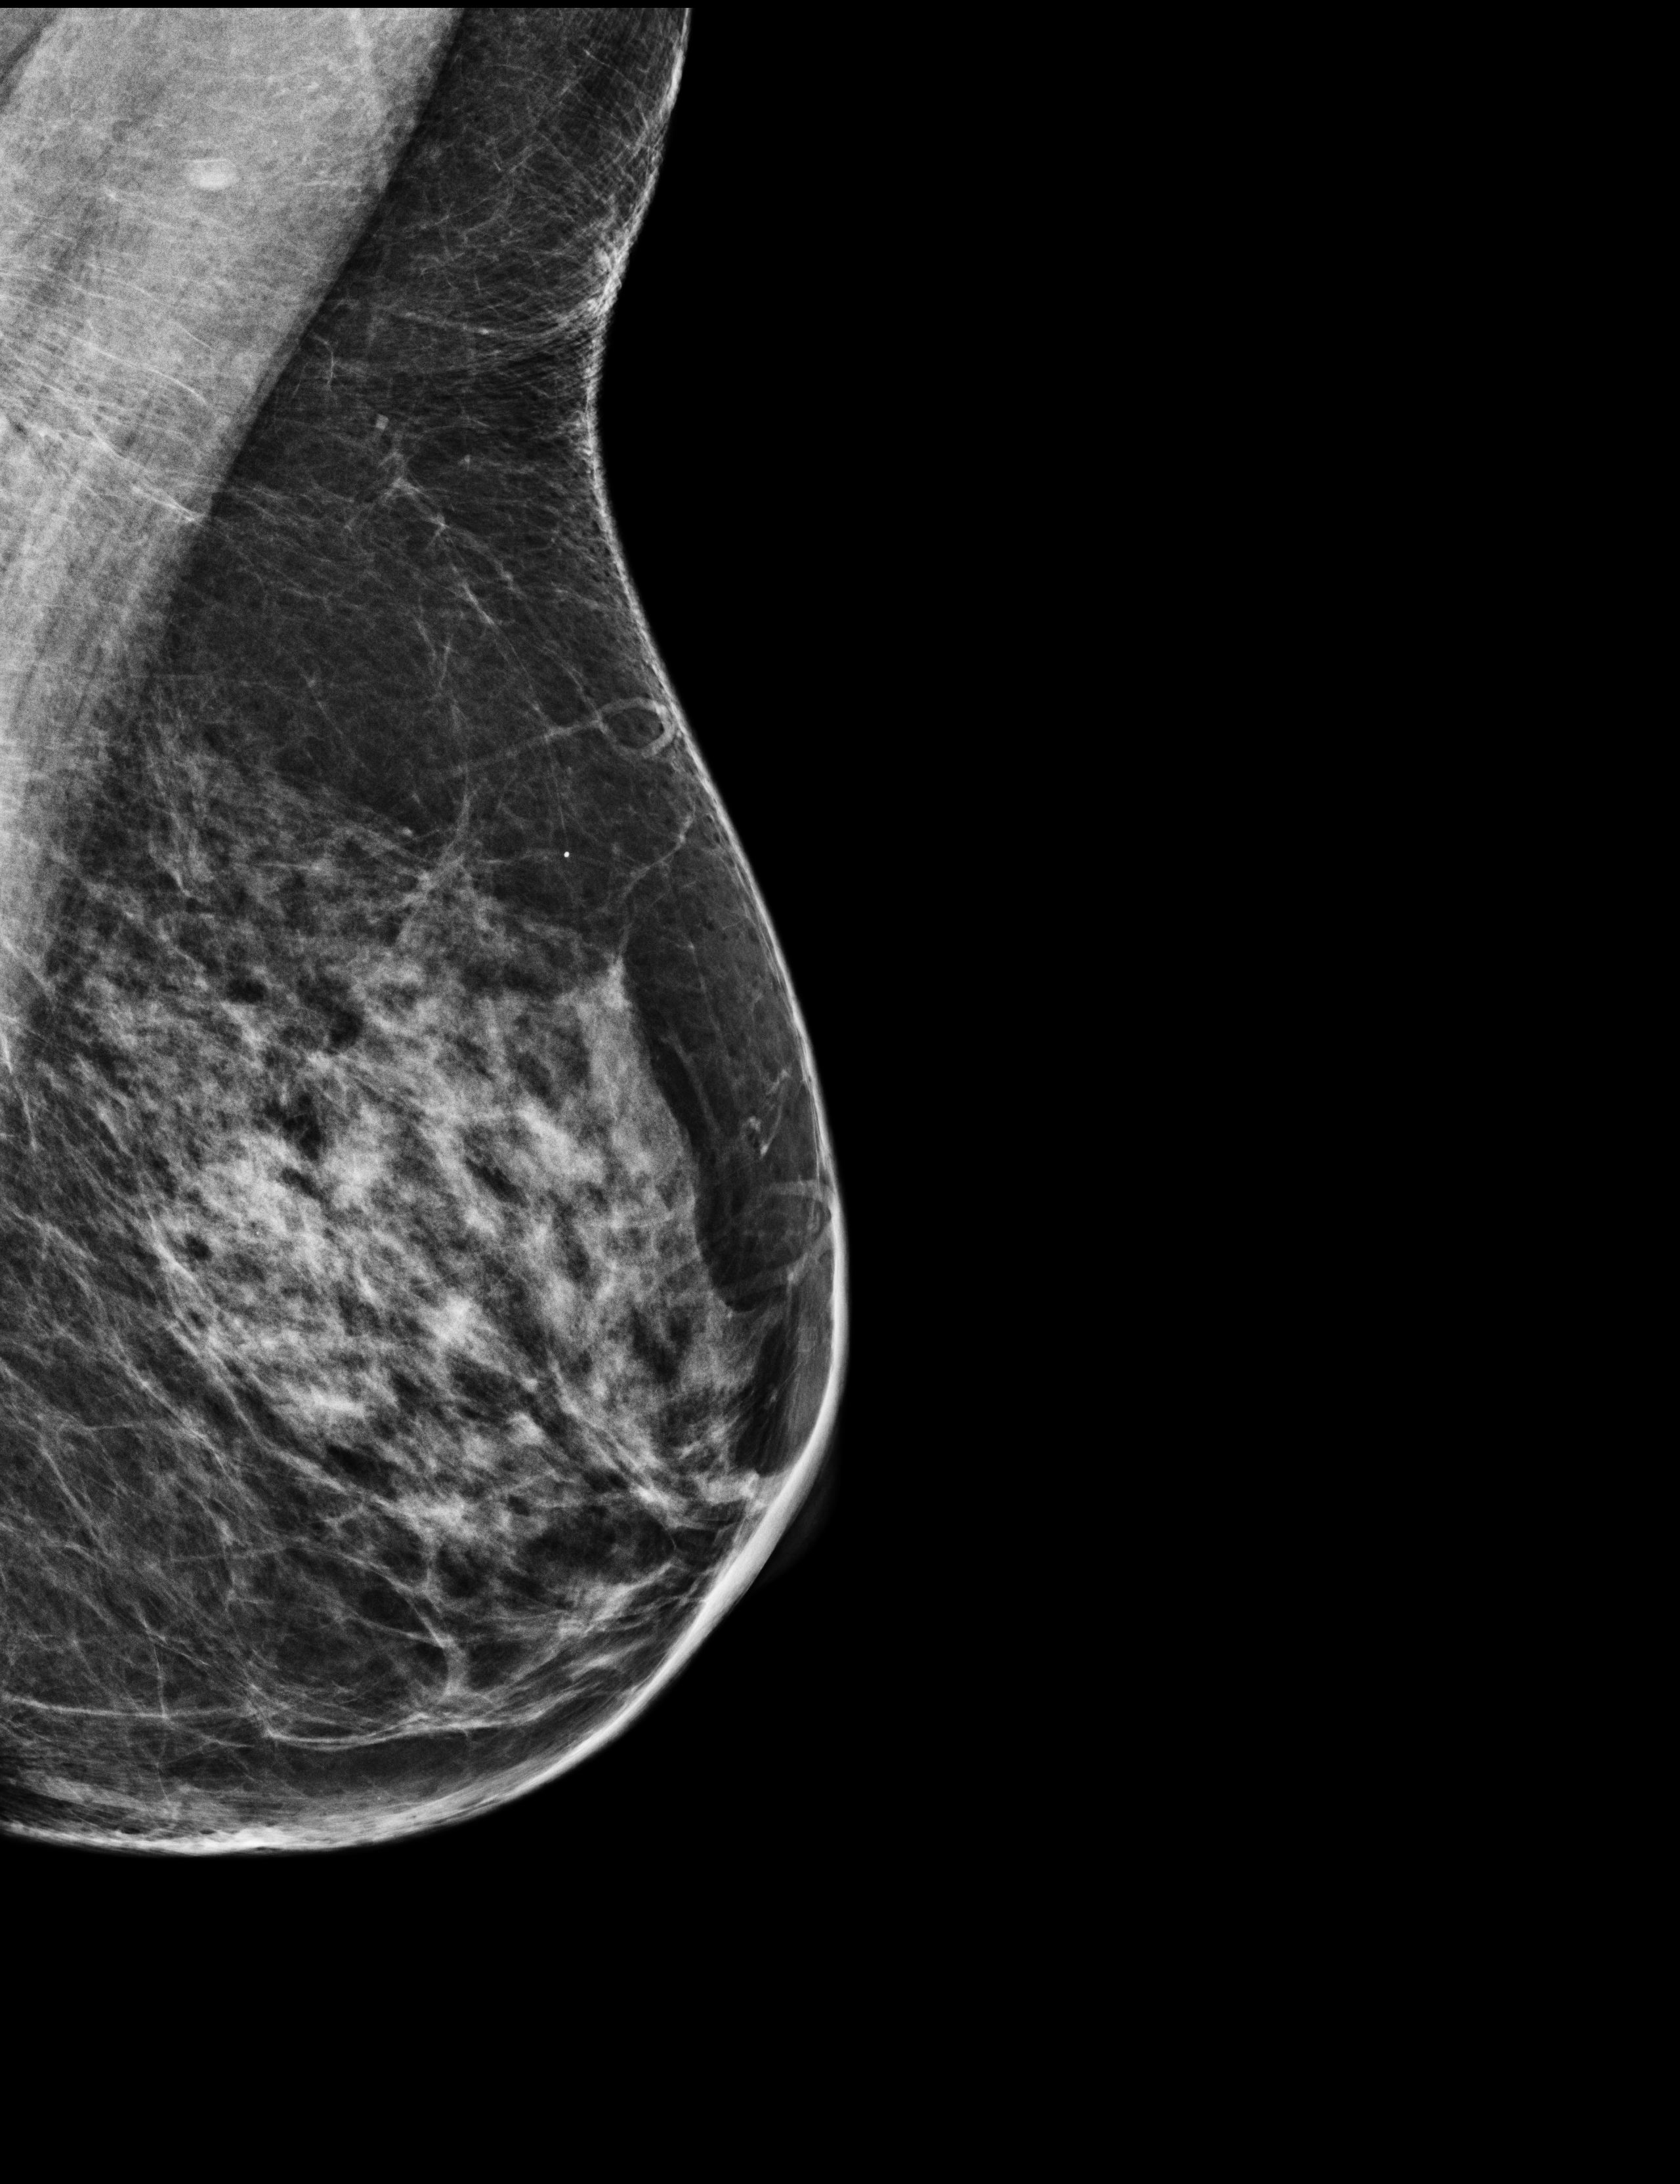
Screening examination; compressed breast thickness 61 mm. Female patient, age 61 years.
Image type: full-field digital mammogram. Breast: left. Projection: mediolateral oblique (MLO) view.